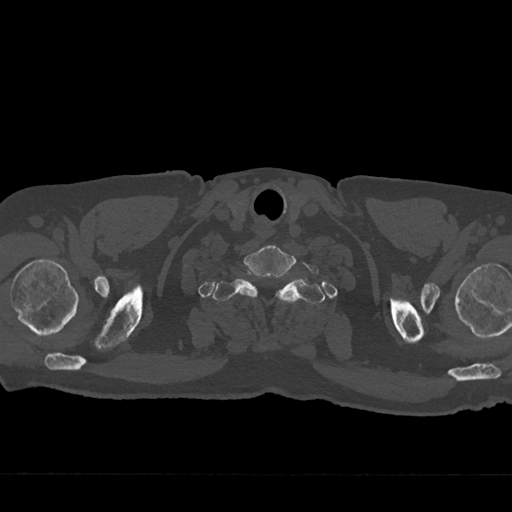
CT including the spine, one axial slice; slice 675 of 797 in the series (ordered by position); reconstruction kernel Br40s/3; 120 kVp; bone window (W 1800 / L 400 HU); 512 × 512 image matrix, field of view 377 × 377 mm. Patient: male, 75 years. From the clinical record (not read from this slice): primary cancer: renal.
Structures marked on this image (semi-automatically segmented with operator editing):
- T1 vertebra: bounding box <213,272,325,304> (left, top, right, bottom; pixels)
- T2 vertebra: <277,292,279,294>